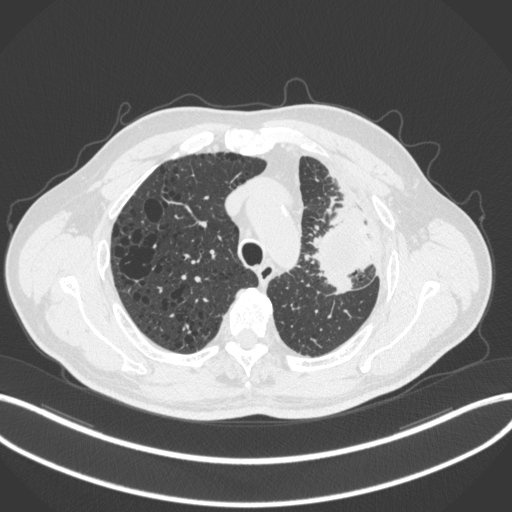
Chest CT, one axial slice. Position 233 of 286 along the scan axis. 120 kVp. Lung window (W 1500 / L -600 HU). 1 mm slice thickness. 512 × 512 image matrix, field of view 400 × 400 mm. Patient: male, 68 years. From the clinical record (not read from this slice): clinical TNM (as recorded): T3 N3 M1.
Annotated regions visible in this slice (rectangle marked by the reading radiologist):
- lung tumour (recorded histology: adenocarcinoma): bounding box <310,195,383,296> (left, top, right, bottom; pixels)